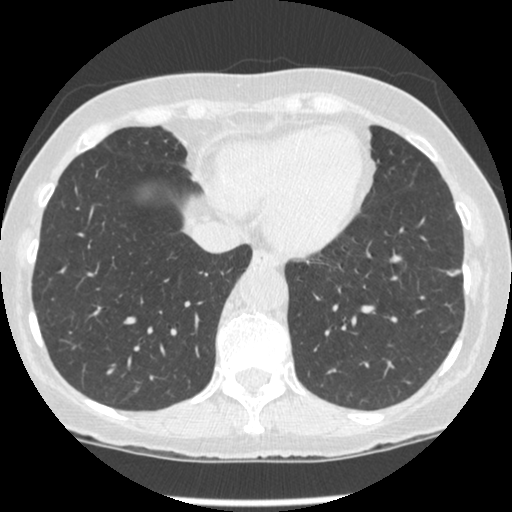
Low-dose screening chest CT, one axial slice; position 69 of 247 along the scan axis; reconstruction kernel STANDARD; 120 kVp; lung window (W 1500 / L -600 HU); 1.25 mm slice thickness; 512 × 512 image matrix.
Outlined on this slice (manually delineated by an expert):
- lesion 1 (tumor, lower lobe of left lung): bounding box <448,272,459,276> (left, top, right, bottom; pixels)